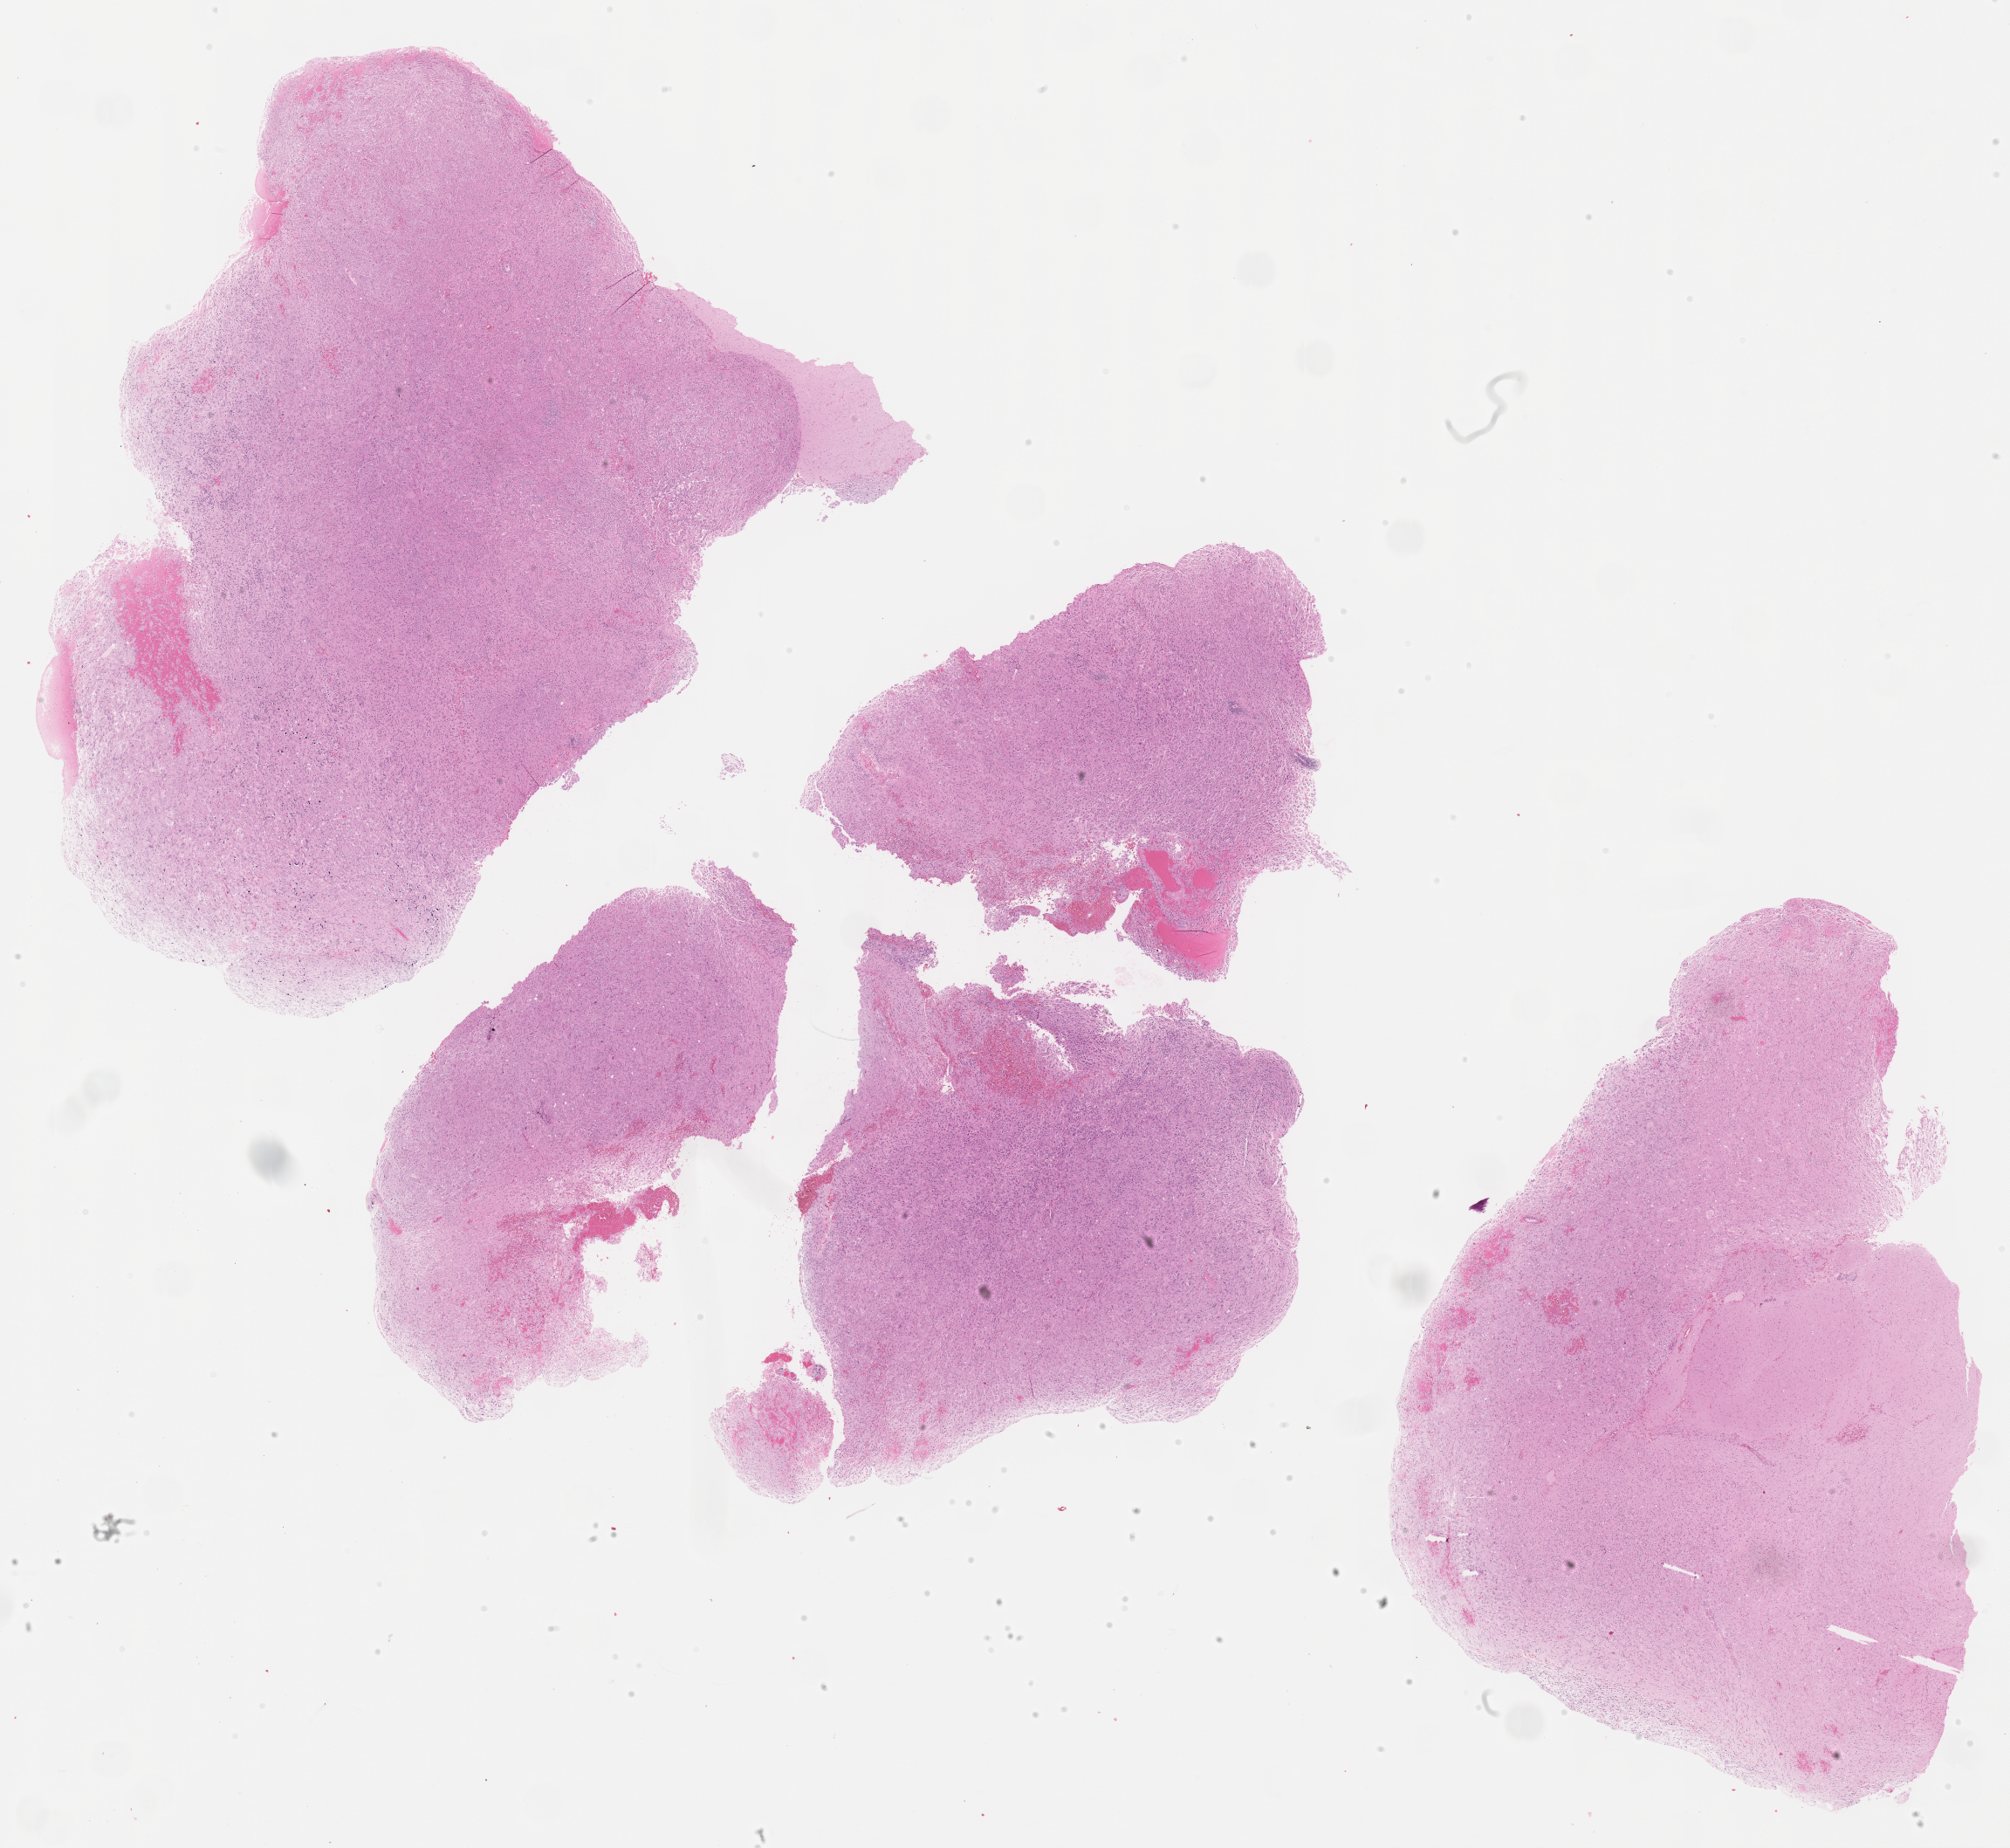
Whole-slide histology image, H&E — whole scanned area (about 18.7 x 17.2 mm, from a 40x scan) shown as a low-resolution overview; formalin-fixed paraffin-embedded (FFPE) diagnostic section; brain, primary tumour sample. Female patient; age at initial diagnosis 44 years.
* diagnosis: Glioblastoma